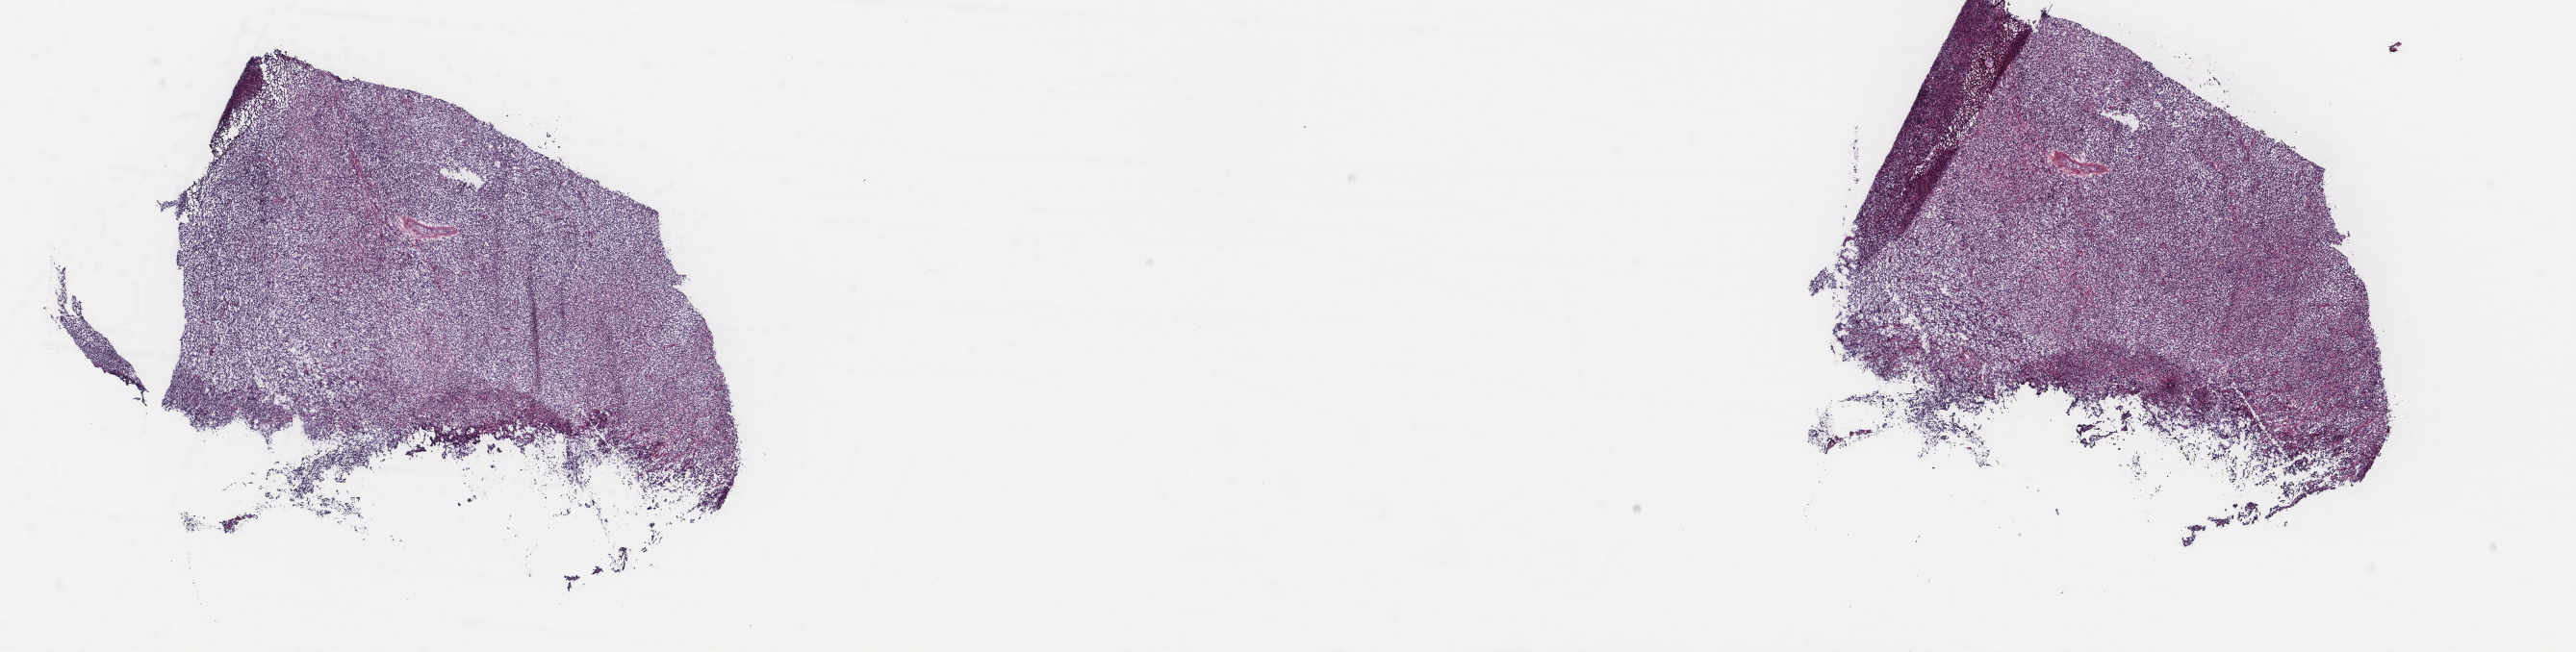
Whole-slide histology image, H&E-stained — low-resolution overview of the scanned area, about 21.2 x 5.4 mm. Frozen section from the top of the tissue portion. Sample: primary tumour, lymphoid tissue. Male, age 40 years at initial diagnosis. Pathologist review of this section (percent, as recorded): tumour cells 95%, tumour nuclei 95%, normal cells 3%, stromal cells 2%, necrosis 0%. Inflammatory infiltration, as recorded: lymphocyte infiltration 3%, monocyte infiltration 1%, neutrophil infiltration 0%.
Pathologic diagnosis: Diffuse large B-cell lymphoma, NOS.